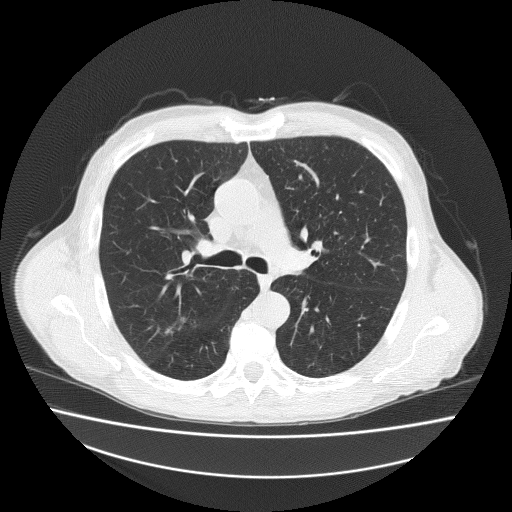
Low-dose screening chest CT, axial slice. Second annual screen. Lung window (W 1500 / L -600 HU). 2 mm slice thickness. Slice 77 of 186 in the series. 512 × 512 image matrix, field of view 408 × 408 mm. Male participant, aged 73 years at enrolment.
• Expert reader's lesion annotation, bounding box <150,308,204,346> (left, top, right, bottom; pixels).
• No non-calcified nodule or mass ≥4 mm was recorded by the screening reader at this exam.